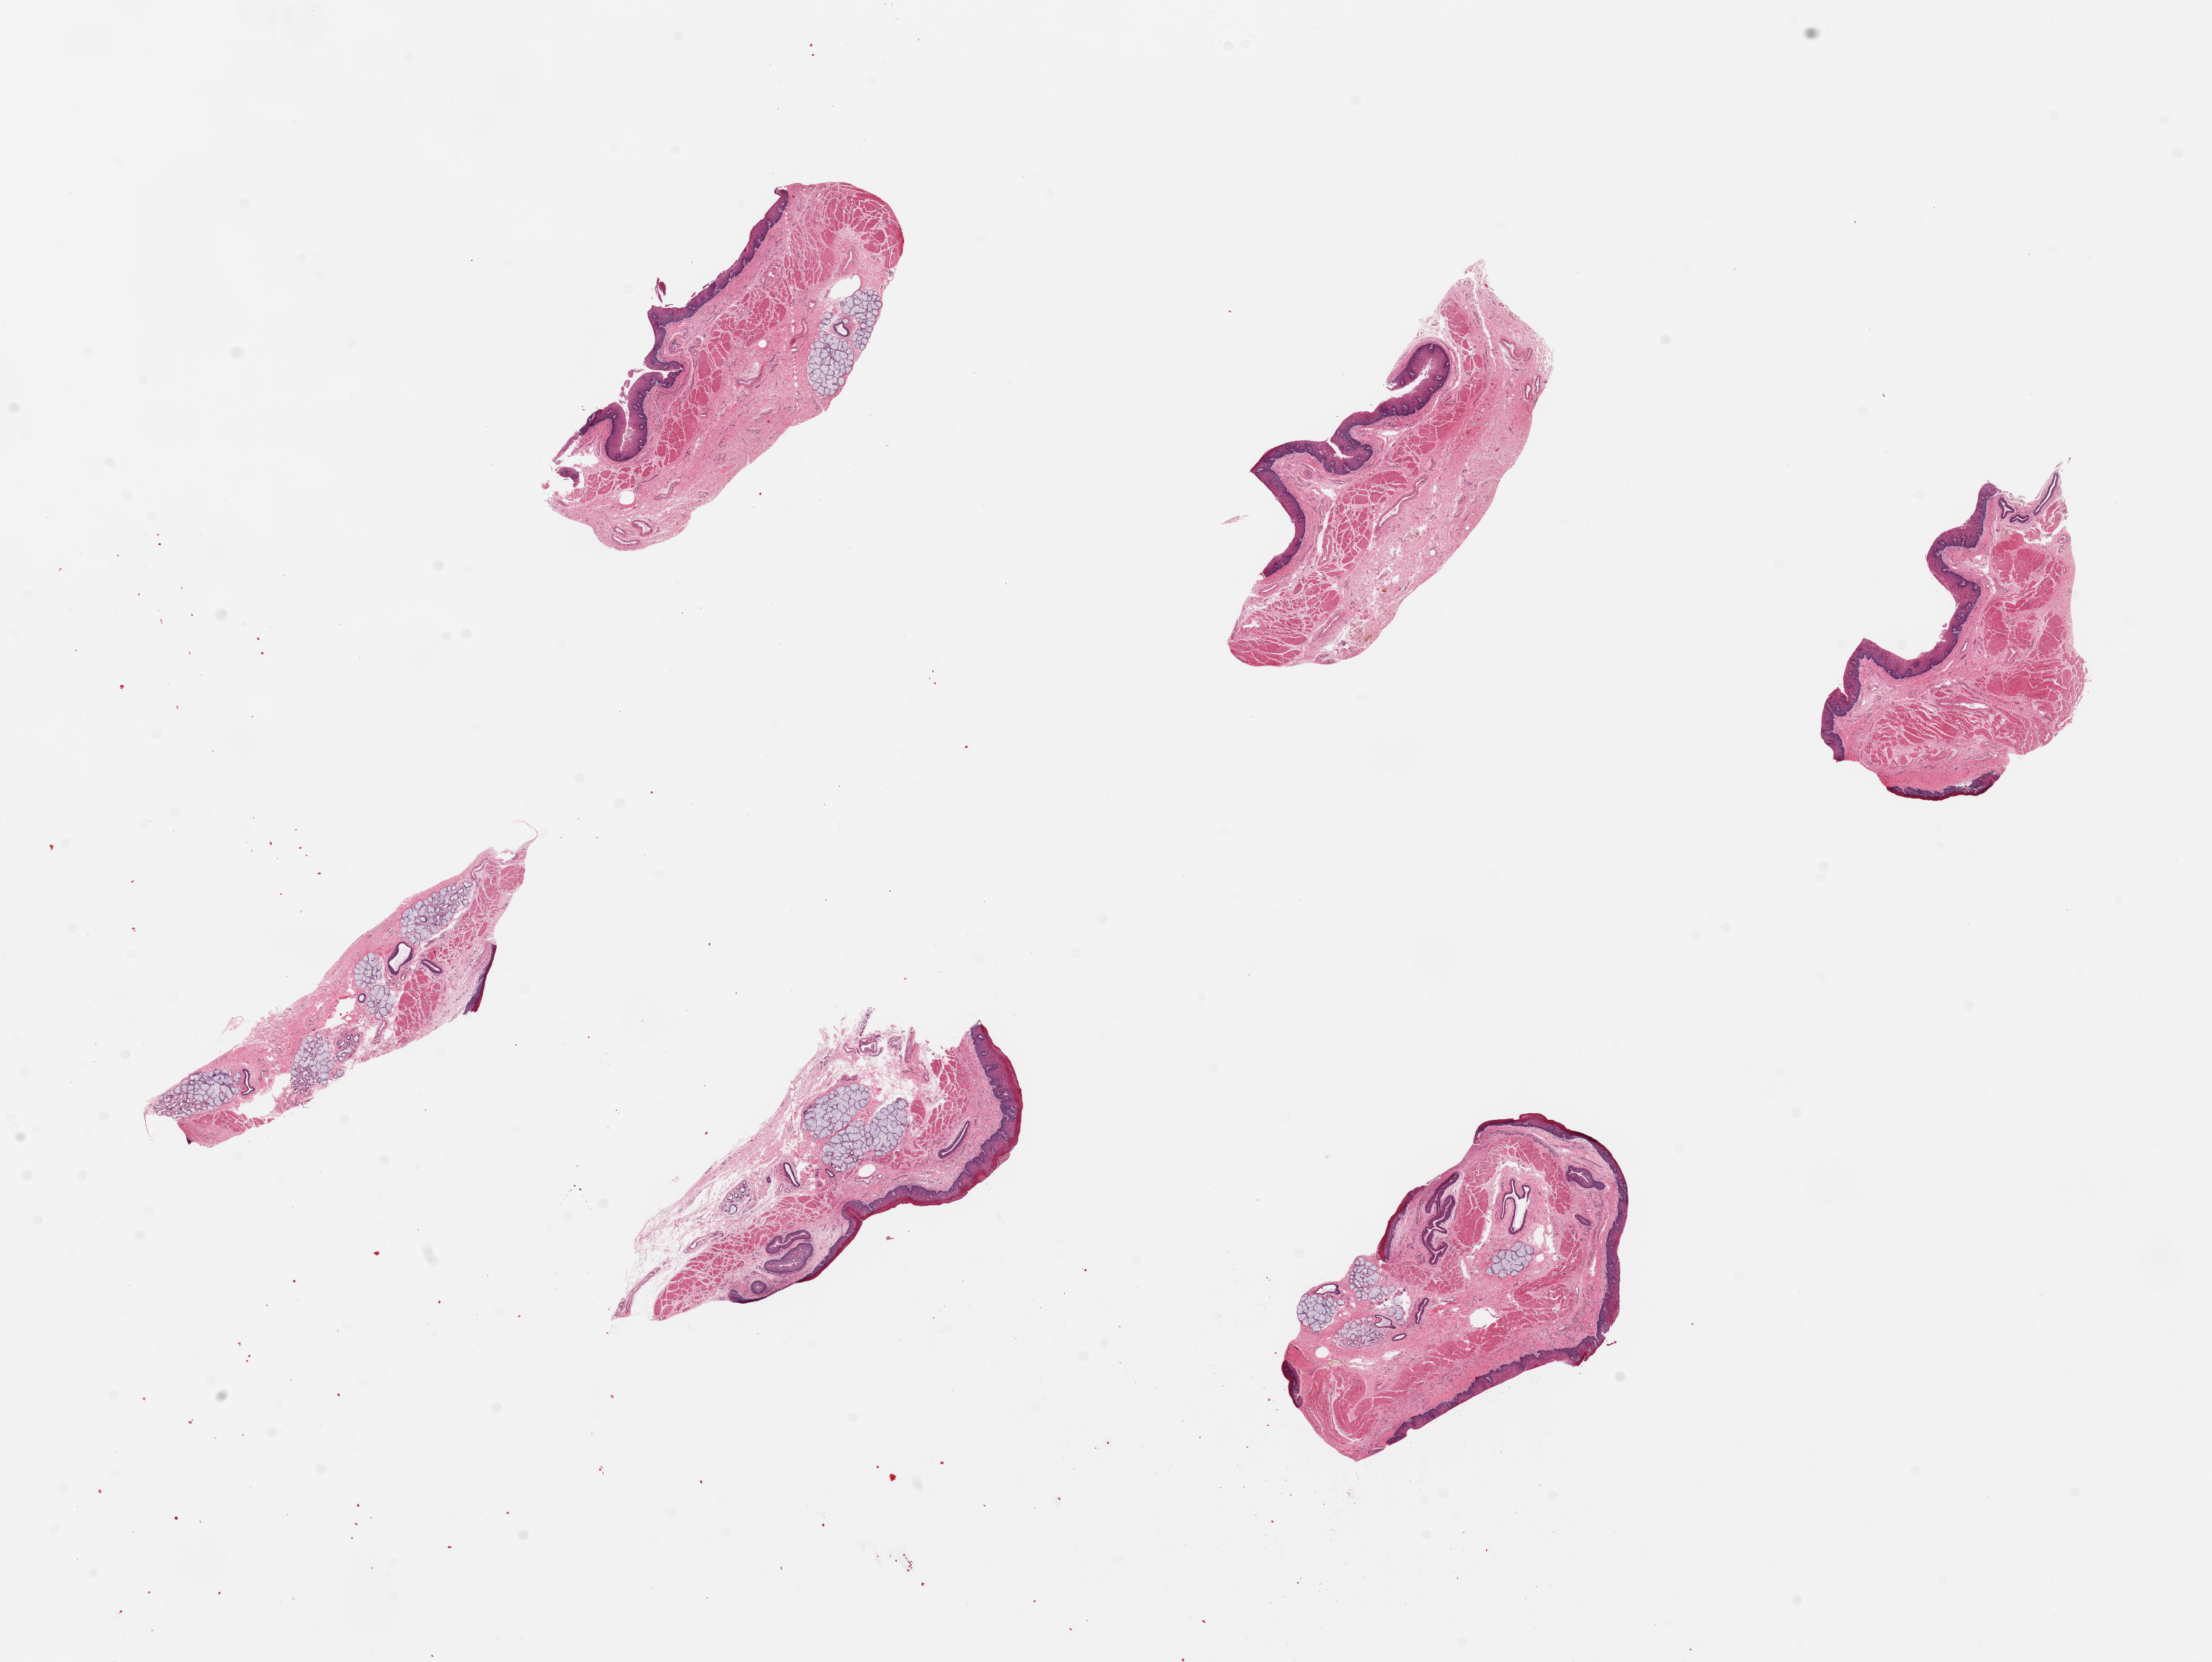
Whole-slide image, H&E stain, brightfield, shown as a low-resolution overview of the whole scanned area (about 23.6 x 17.7 mm, acquisition: 20x scan); PAXgene-fixed paraffin-embedded (PFPE) section; sampled site (target tissue): esophageal mucous membrane; tissue donor sample. Donor sex: female.
Pathologist's review note for this sample: 6 pieces; Squamous mucosa is 5-10% thickness; Submucosa mucous glands present.